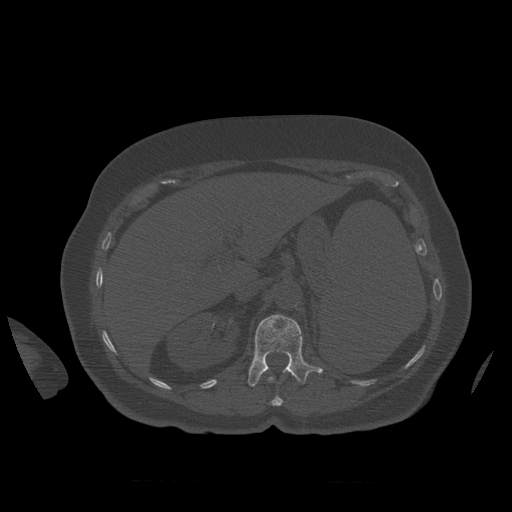
CT including the spine, one axial slice; position 284 of 399 along the scan axis; bone window (W 1800 / L 400 HU); 1.25 mm slice thickness; 512 × 512 image matrix. Patient age 81 years. Case-level facts recorded for this patient, not image findings: primary cancer: renal.
Structures marked on this image (semi-automatically segmented with operator editing):
- L1 vertebra: bounding box (x1, y1, x2, y2) in pixels: (248, 315, 324, 387)
- T12 vertebra: (269, 378, 284, 406)